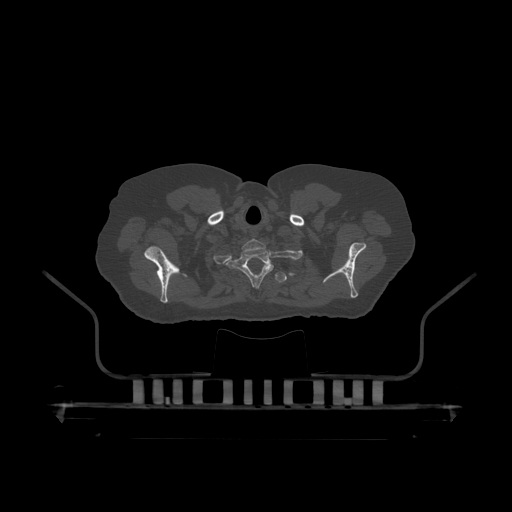
CT including the spine, one axial slice; reconstruction kernel STANDARD; bone window (W 1800 / L 400 HU); 1.25 mm slice thickness; 512 × 512 image matrix, field of view 650 × 650 mm. Patient: male, 60 years. Case-level facts recorded for this patient, not image findings: primary cancer: prostate.
Outlined on this slice (semi-automatic segmentation, software-assisted and operator-edited):
- T1 vertebra: bounding box [x1, y1, x2, y2] px = [228, 240, 274, 288]
- T2 vertebra: [274, 271, 287, 284]